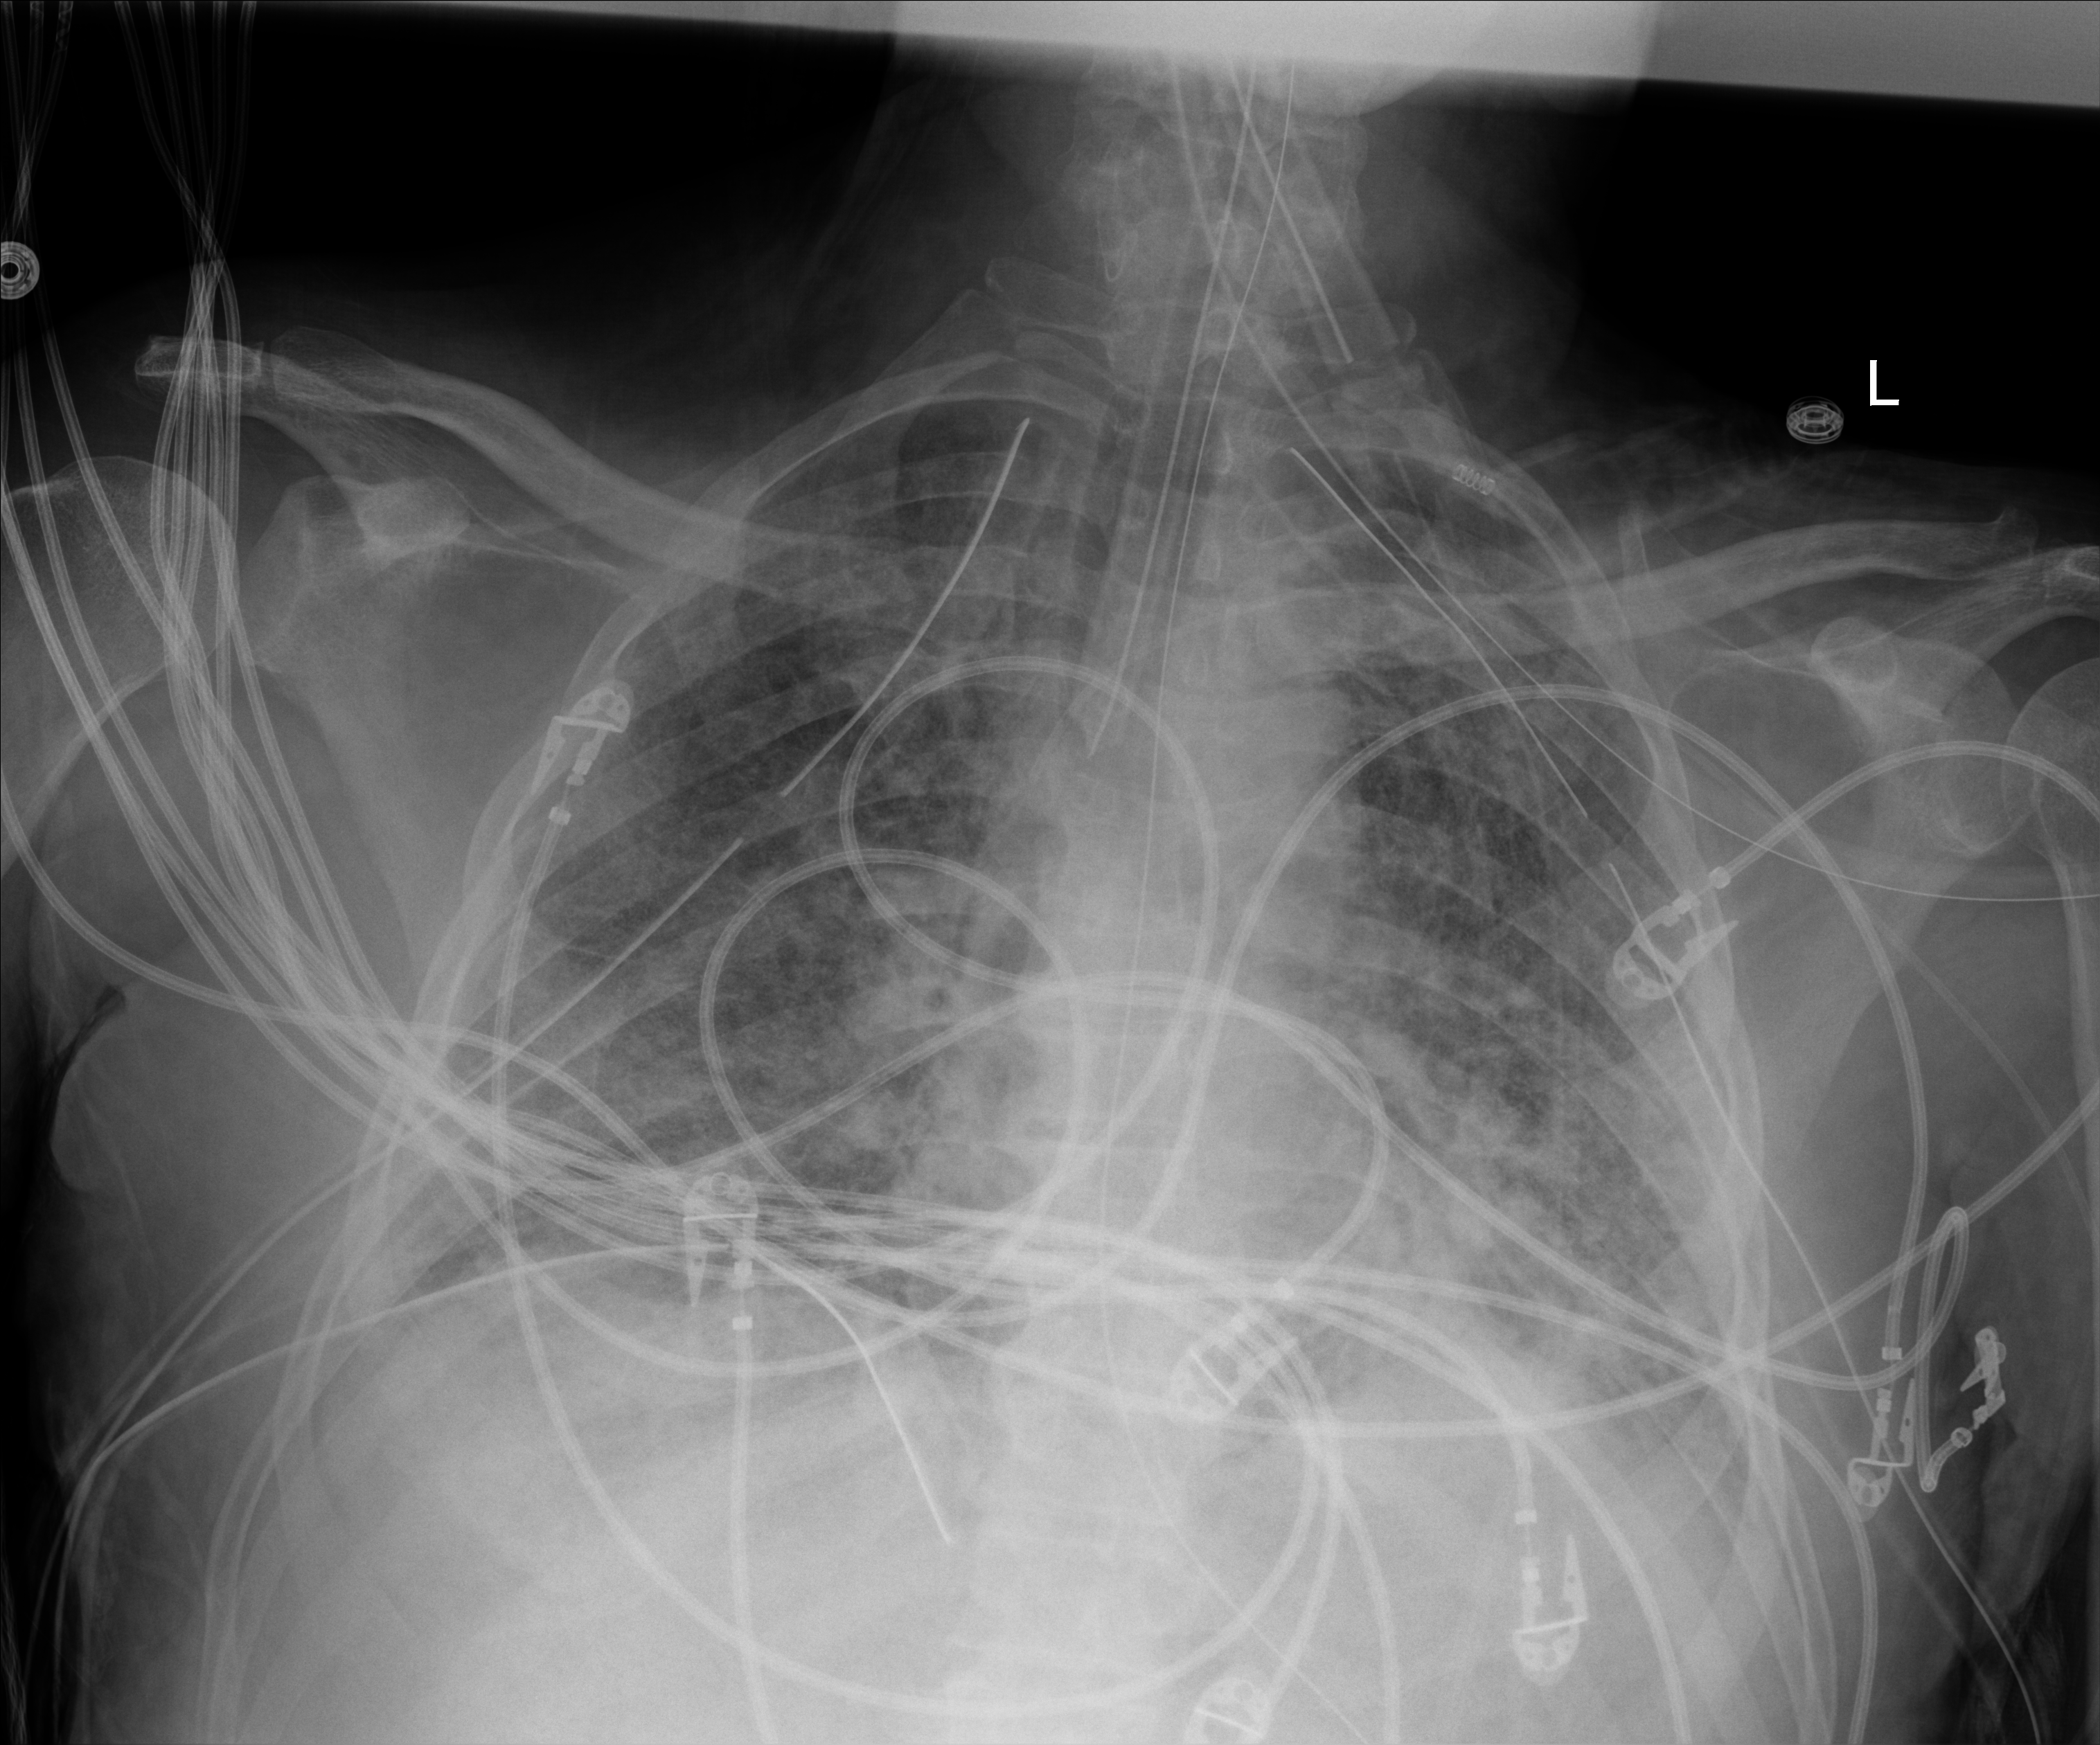
Portable chest radiograph; anteroposterior (AP) projection. Patient hospitalised with COVID-19; male, aged 18–59 years.
Admission-level facts for this patient (not findings on this image; timing relative to this image not recorded): COPD (admission record): no; diabetes (admission record): no.